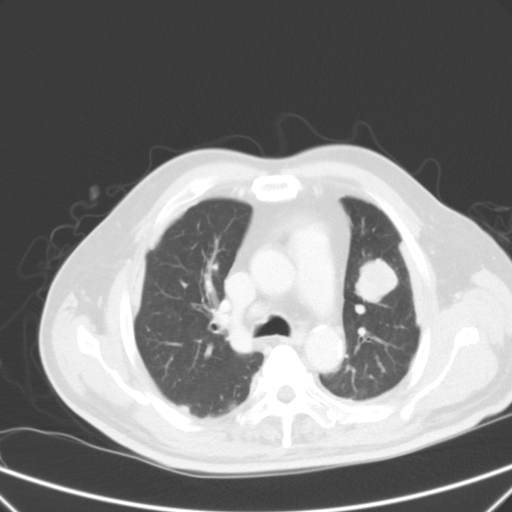
Chest CT, one axial slice; 120 kVp; intravenous contrast given; lung window (W 1500 / L -600 HU); 5 mm slice thickness; 512 × 512 image matrix. Patient: male, 66 years. Case-level facts recorded for this patient, not image findings: clinical TNM (as recorded): T1c N3 M1a.
Outlined on this slice (rectangle marked by the reading radiologist):
- lung tumour (recorded histology: squamous cell carcinoma): box from (x=350, y=258) to (x=402, y=309) px